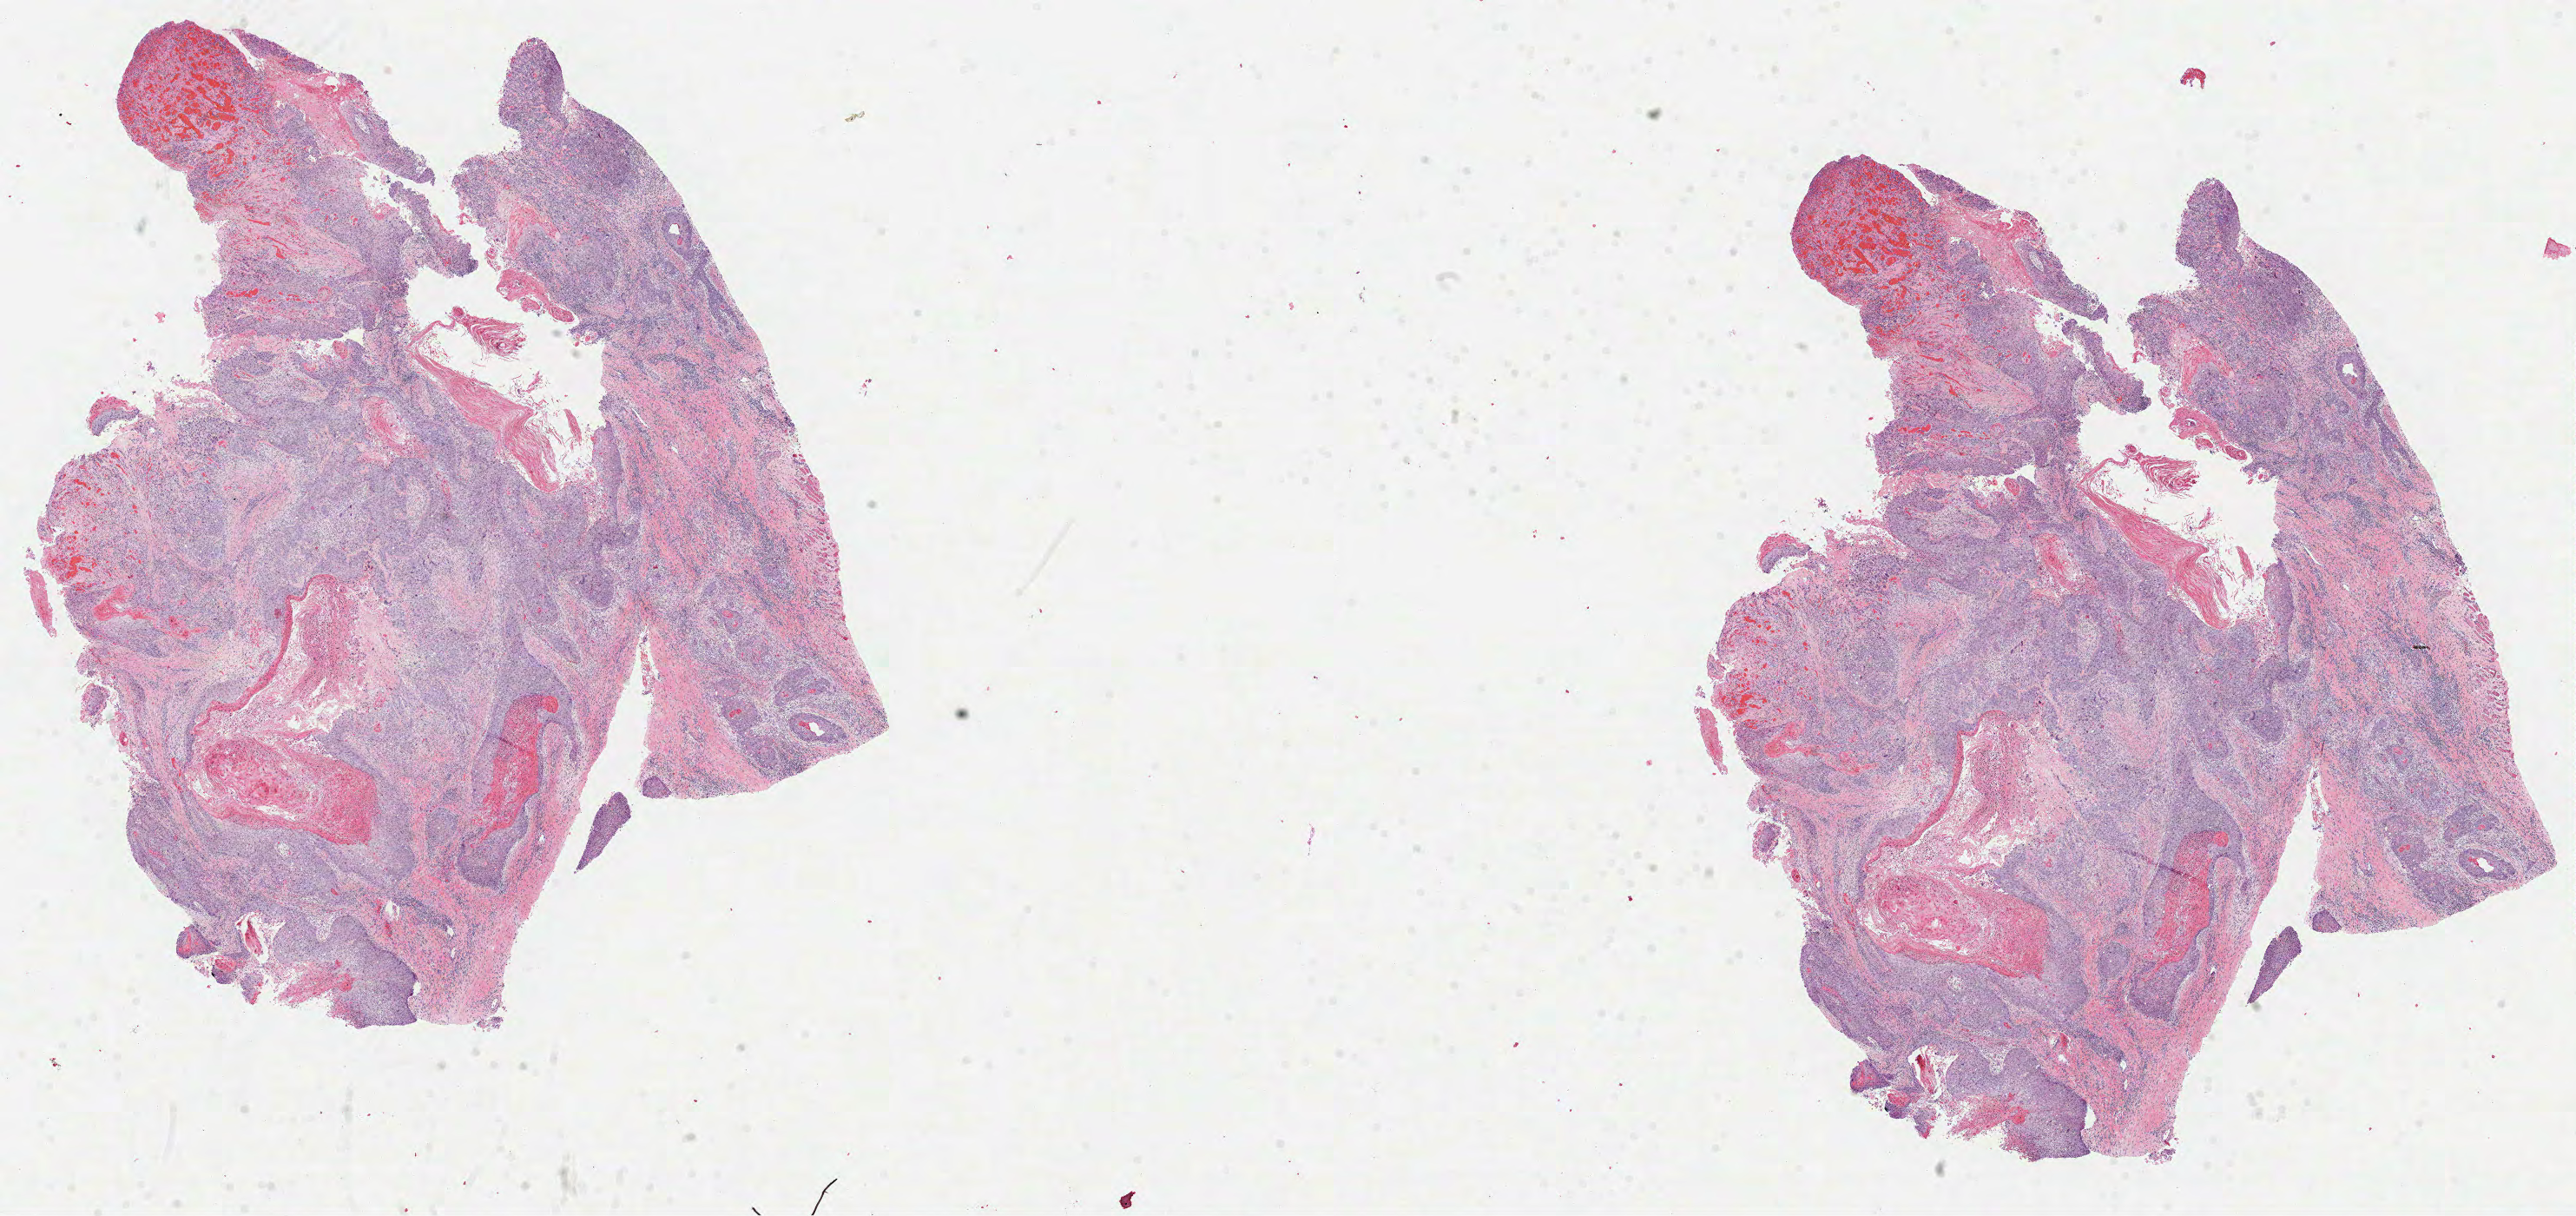
H&E-stained whole-slide image — shown as a low-resolution overview of the whole scanned area (about 23.9 x 11.3 mm). Formalin-fixed paraffin-embedded (FFPE) diagnostic section. Head and neck, primary tumour sample. Female patient; age at initial diagnosis 85 years. Histologic grade: G2 (moderately differentiated).
* TNM: T4a N2b
* histologic diagnosis: Squamous cell carcinoma, NOS (overlapping lesion of lip, oral cavity and pharynx)
* AJCC pathologic stage: IVA